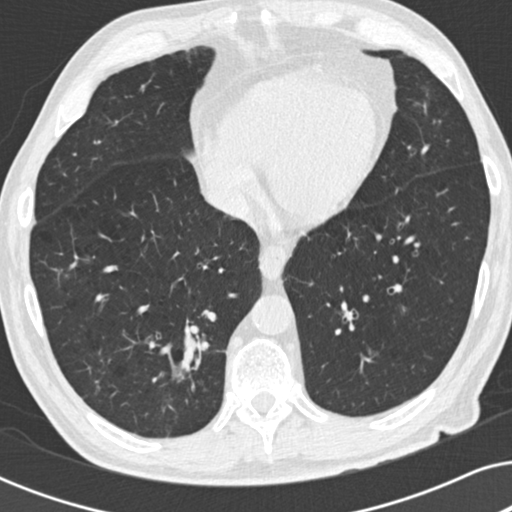
Chest CT (low-dose screening protocol), one axial image, first (baseline) screen, lung window (W 1500 / L -600 HU), slice 114 of 191 in the series. Male participant, aged 73 years at enrolment. Current smoker at enrolment.
Expert reader's lesion annotation, box from (x=153, y=291) to (x=226, y=373) px. The screening reader recorded 2 non-calcified nodules or masses ≥4 mm on this exam (right lower lobe, right upper lobe); which of them this box marks is not recorded. Official screen result: positive, change unspecified: nodule(s) >= 4 mm or enlarging nodule(s), mass(es), or other non-specific abnormalities suspicious for lung cancer. Later outcome: lung cancer diagnosed 63 days after this screen — carcinoid tumor, NOS, right lower lobe, carcinoid, stage not assessed, 12 mm at pathology.